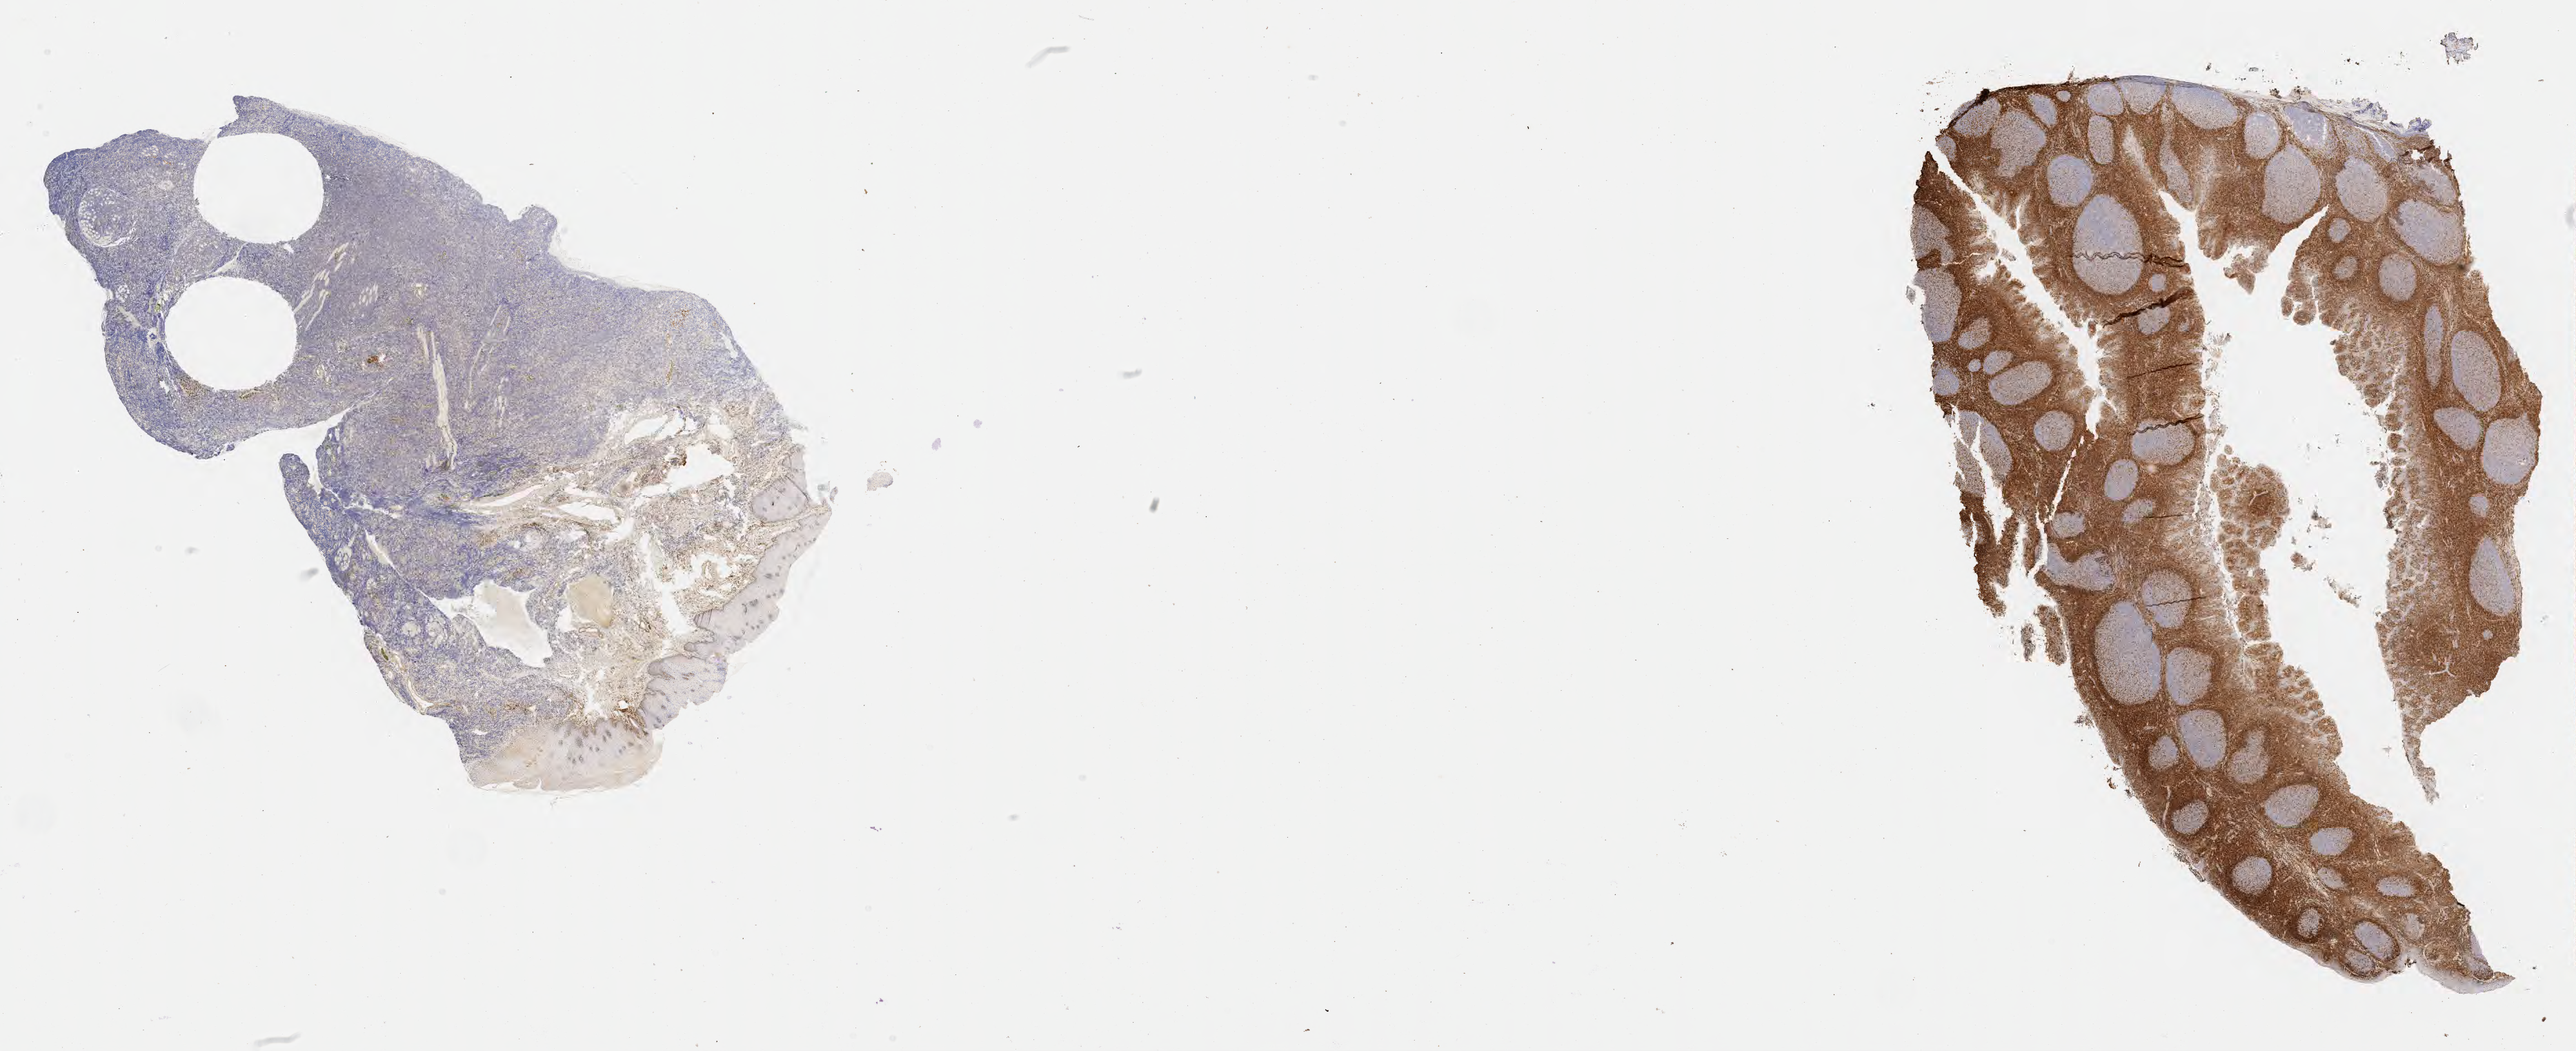
IHC for BCL2, whole-slide image — low-resolution overview of the scanned area, about 30.2 x 12.3 mm; specimen: tumor tissue; anatomic site: cranium. Patient: male, age at initial diagnosis 6 years.
* histologic diagnosis: Burkitt lymphoma, NOS